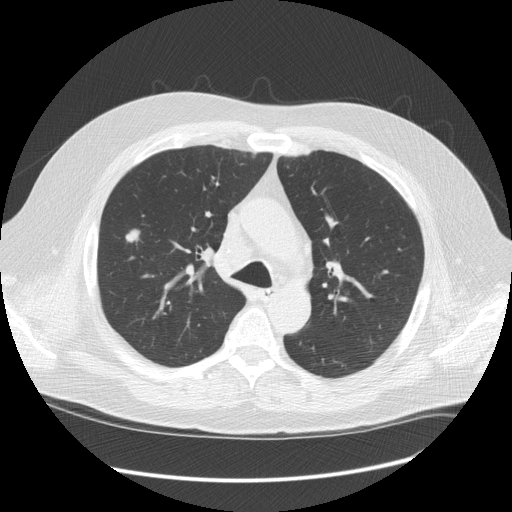
Chest CT (low-dose screening protocol), one axial image, third screening round (two years after baseline), lung window (W 1500 / L -600 HU), 2.5 mm slice thickness, slice 40 of 128 in the series, 512 × 512 image matrix. Male participant, aged 61 years at enrolment.
• Lesion marked by an expert reader, bounding box [x1, y1, x2, y2] px = [106, 218, 151, 256].
• Reader record for this screening exam (exam-level; its link to the box is not recorded): non-calcified nodule or mass ≥4 mm, right upper lobe, 13 × 11 mm, spiculated (stellate) margins, soft tissue attenuation, pre-existing on the prior screen: yes; interval growth: yes.
• Official screen result: positive, other.
• Lung cancer was diagnosed 21 days after this screen: adenocarcinoma, NOS, right upper lobe, stage IIIA (AJCC 6th edition), 13 mm at pathology.